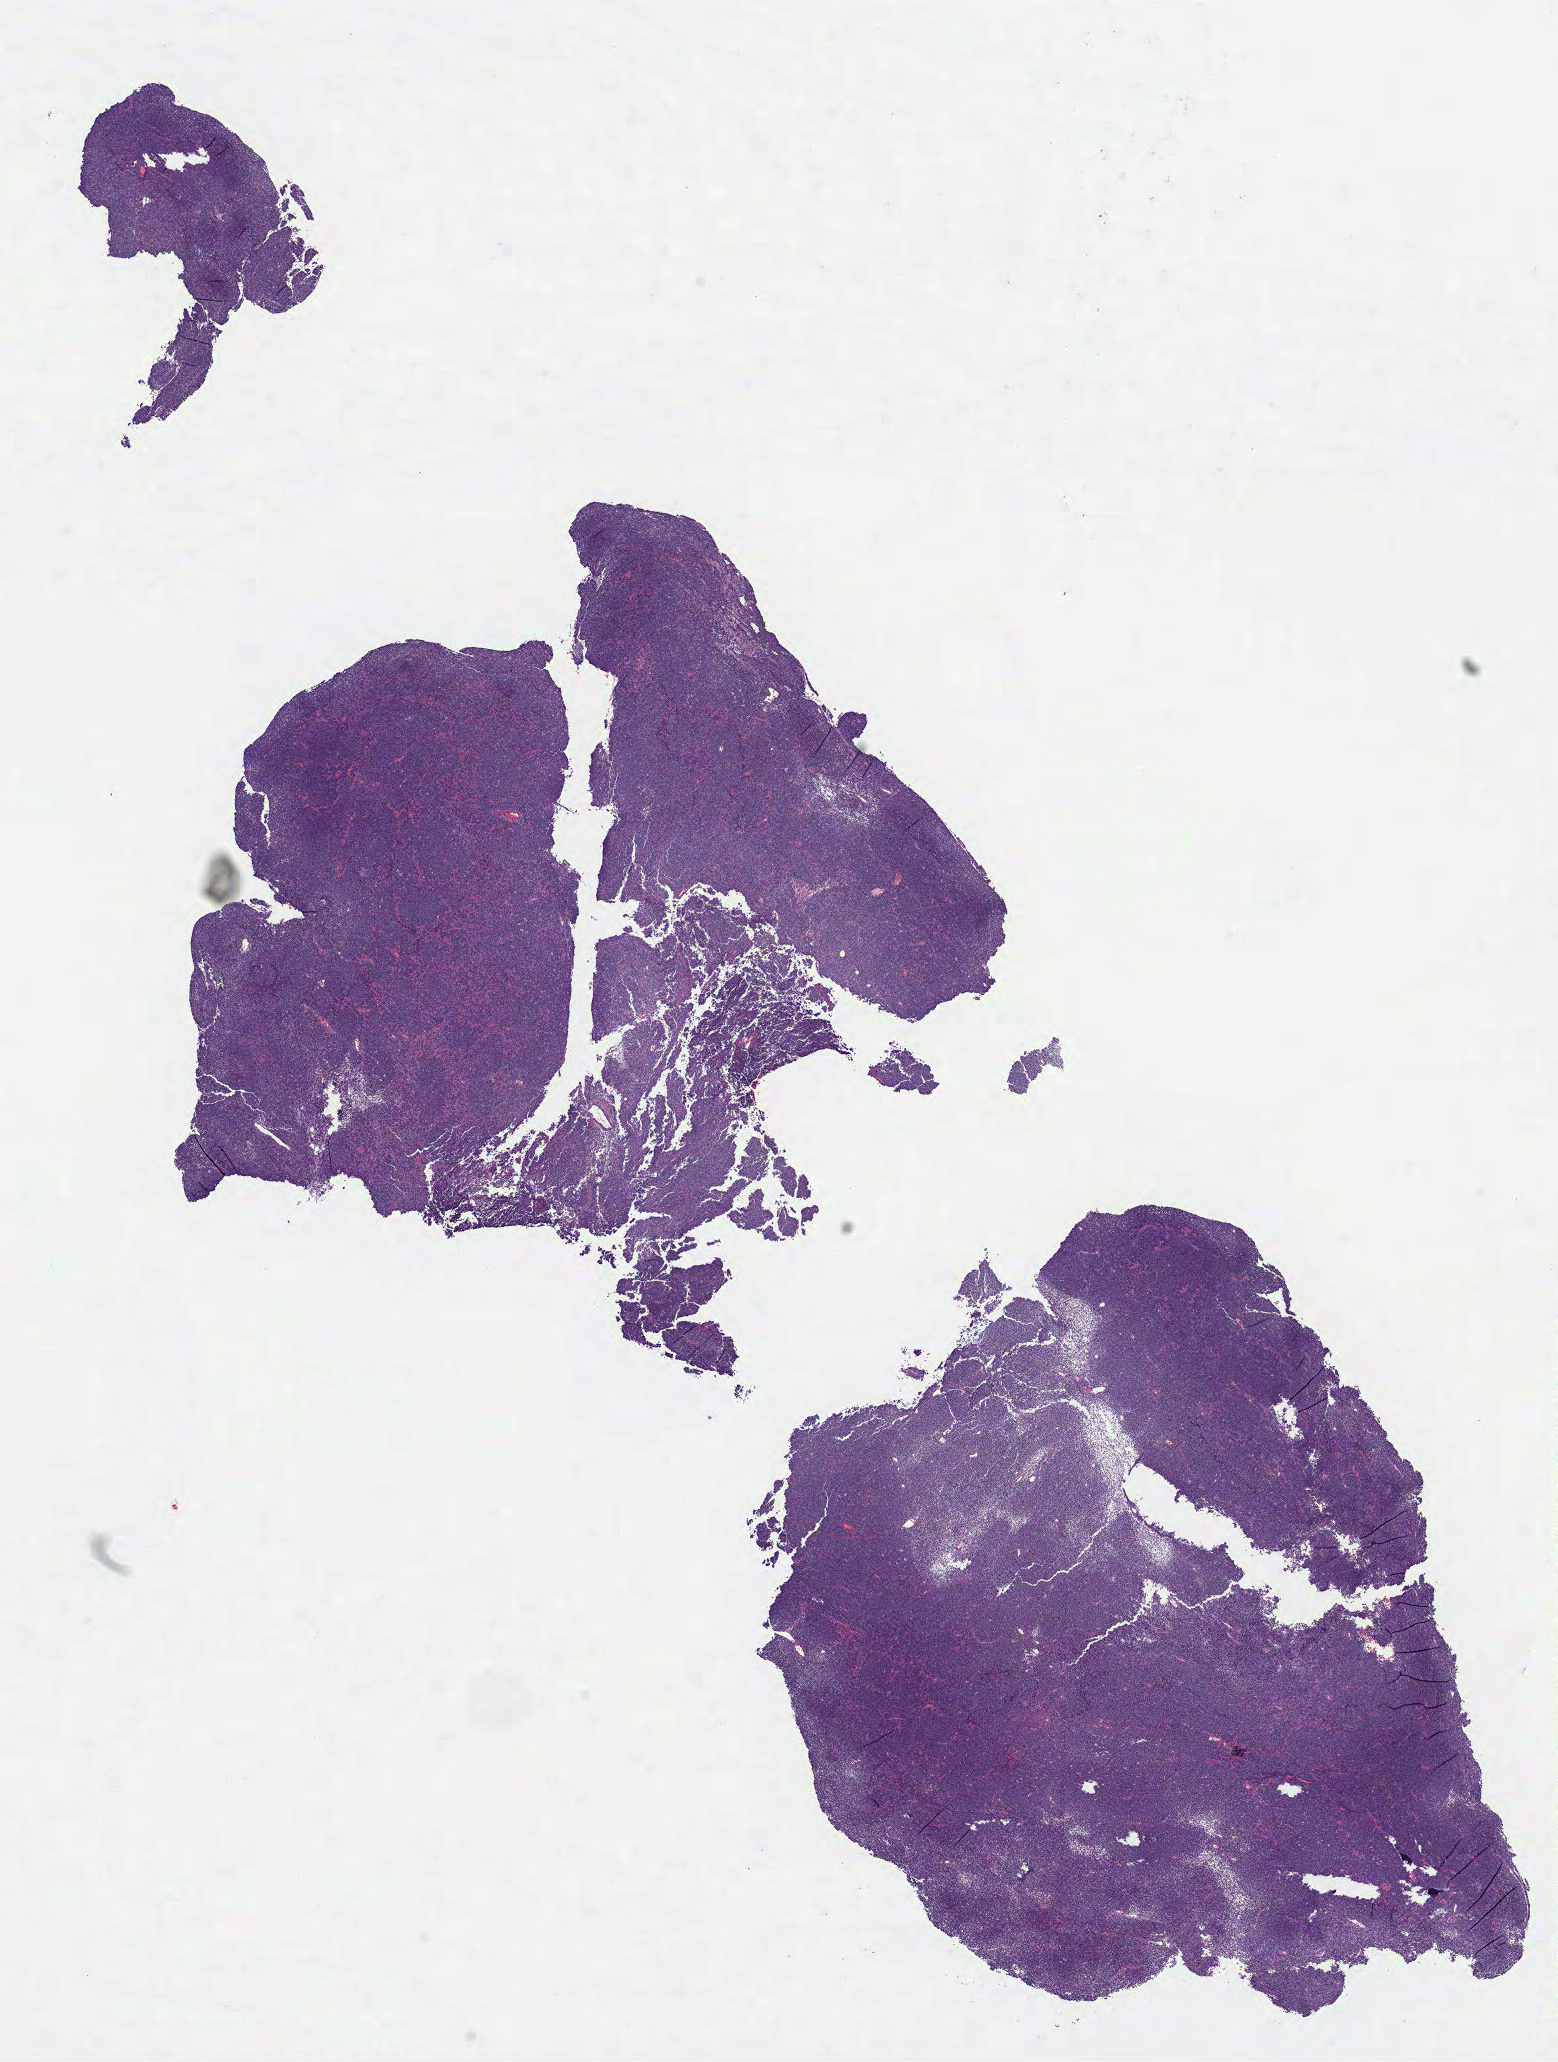
H&E whole-slide image — a low-resolution overview of the entire scanned area, about 12.6 x 16.6 mm (acquisition: 40x scan); formalin-fixed paraffin-embedded (FFPE) diagnostic section; sample: primary tumour, connective, subcutaneous and other soft tissues. Female, age 31 years at initial diagnosis.
Diagnosis: Synovial sarcoma, NOS.